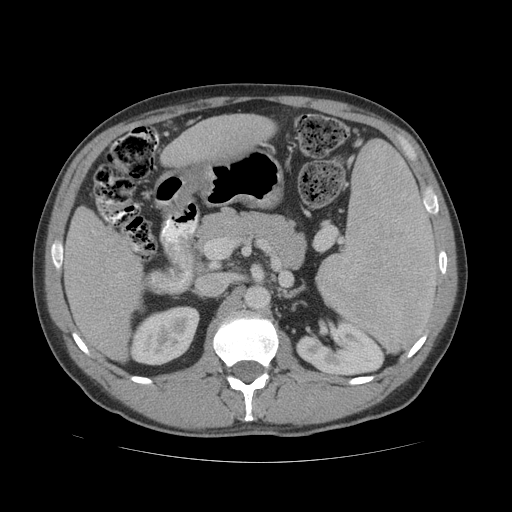
Contrast-enhanced abdominal CT (liver protocol), one axial slice; slice 25 of 81 in the series (ordered by position); soft-tissue window (W 400 / L 40 HU); 2.5 mm slice thickness; 512 × 512 image matrix. From the clinical record (not read from this slice): diagnosis: hepatocellular carcinoma (patient treated with transarterial chemoembolisation; whether this scan precedes or follows treatment is not stated here); TNM stage (as recorded): Stage-IVB.
Outlined on this slice (semi-automatic segmentation, software-assisted and operator-edited):
- liver parenchyma outside the tumour (the mass and vessels are separate outlines, so this box may not span the whole liver): box from (x=62, y=114) to (x=274, y=360) px